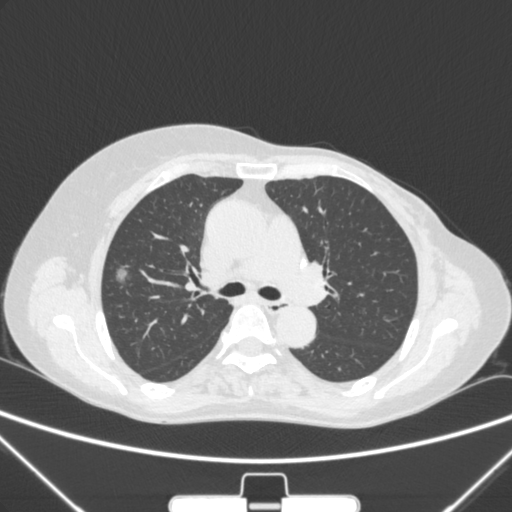
Chest CT, one axial slice; position 162 of 265 along the scan axis; lung window (W 1500 / L -600 HU); 1 mm slice thickness; 512 × 512 image matrix, field of view 350 × 350 mm. Patient: female, 64 years. Case-level facts recorded for this patient, not image findings: clinical TNM (as recorded): T1c N0 M0; histopathological grade: G1-2.
Structures marked on this image (rectangle marked by the reading radiologist):
- lung tumour (recorded histology: adenocarcinoma): box from (x=108, y=260) to (x=140, y=298) px